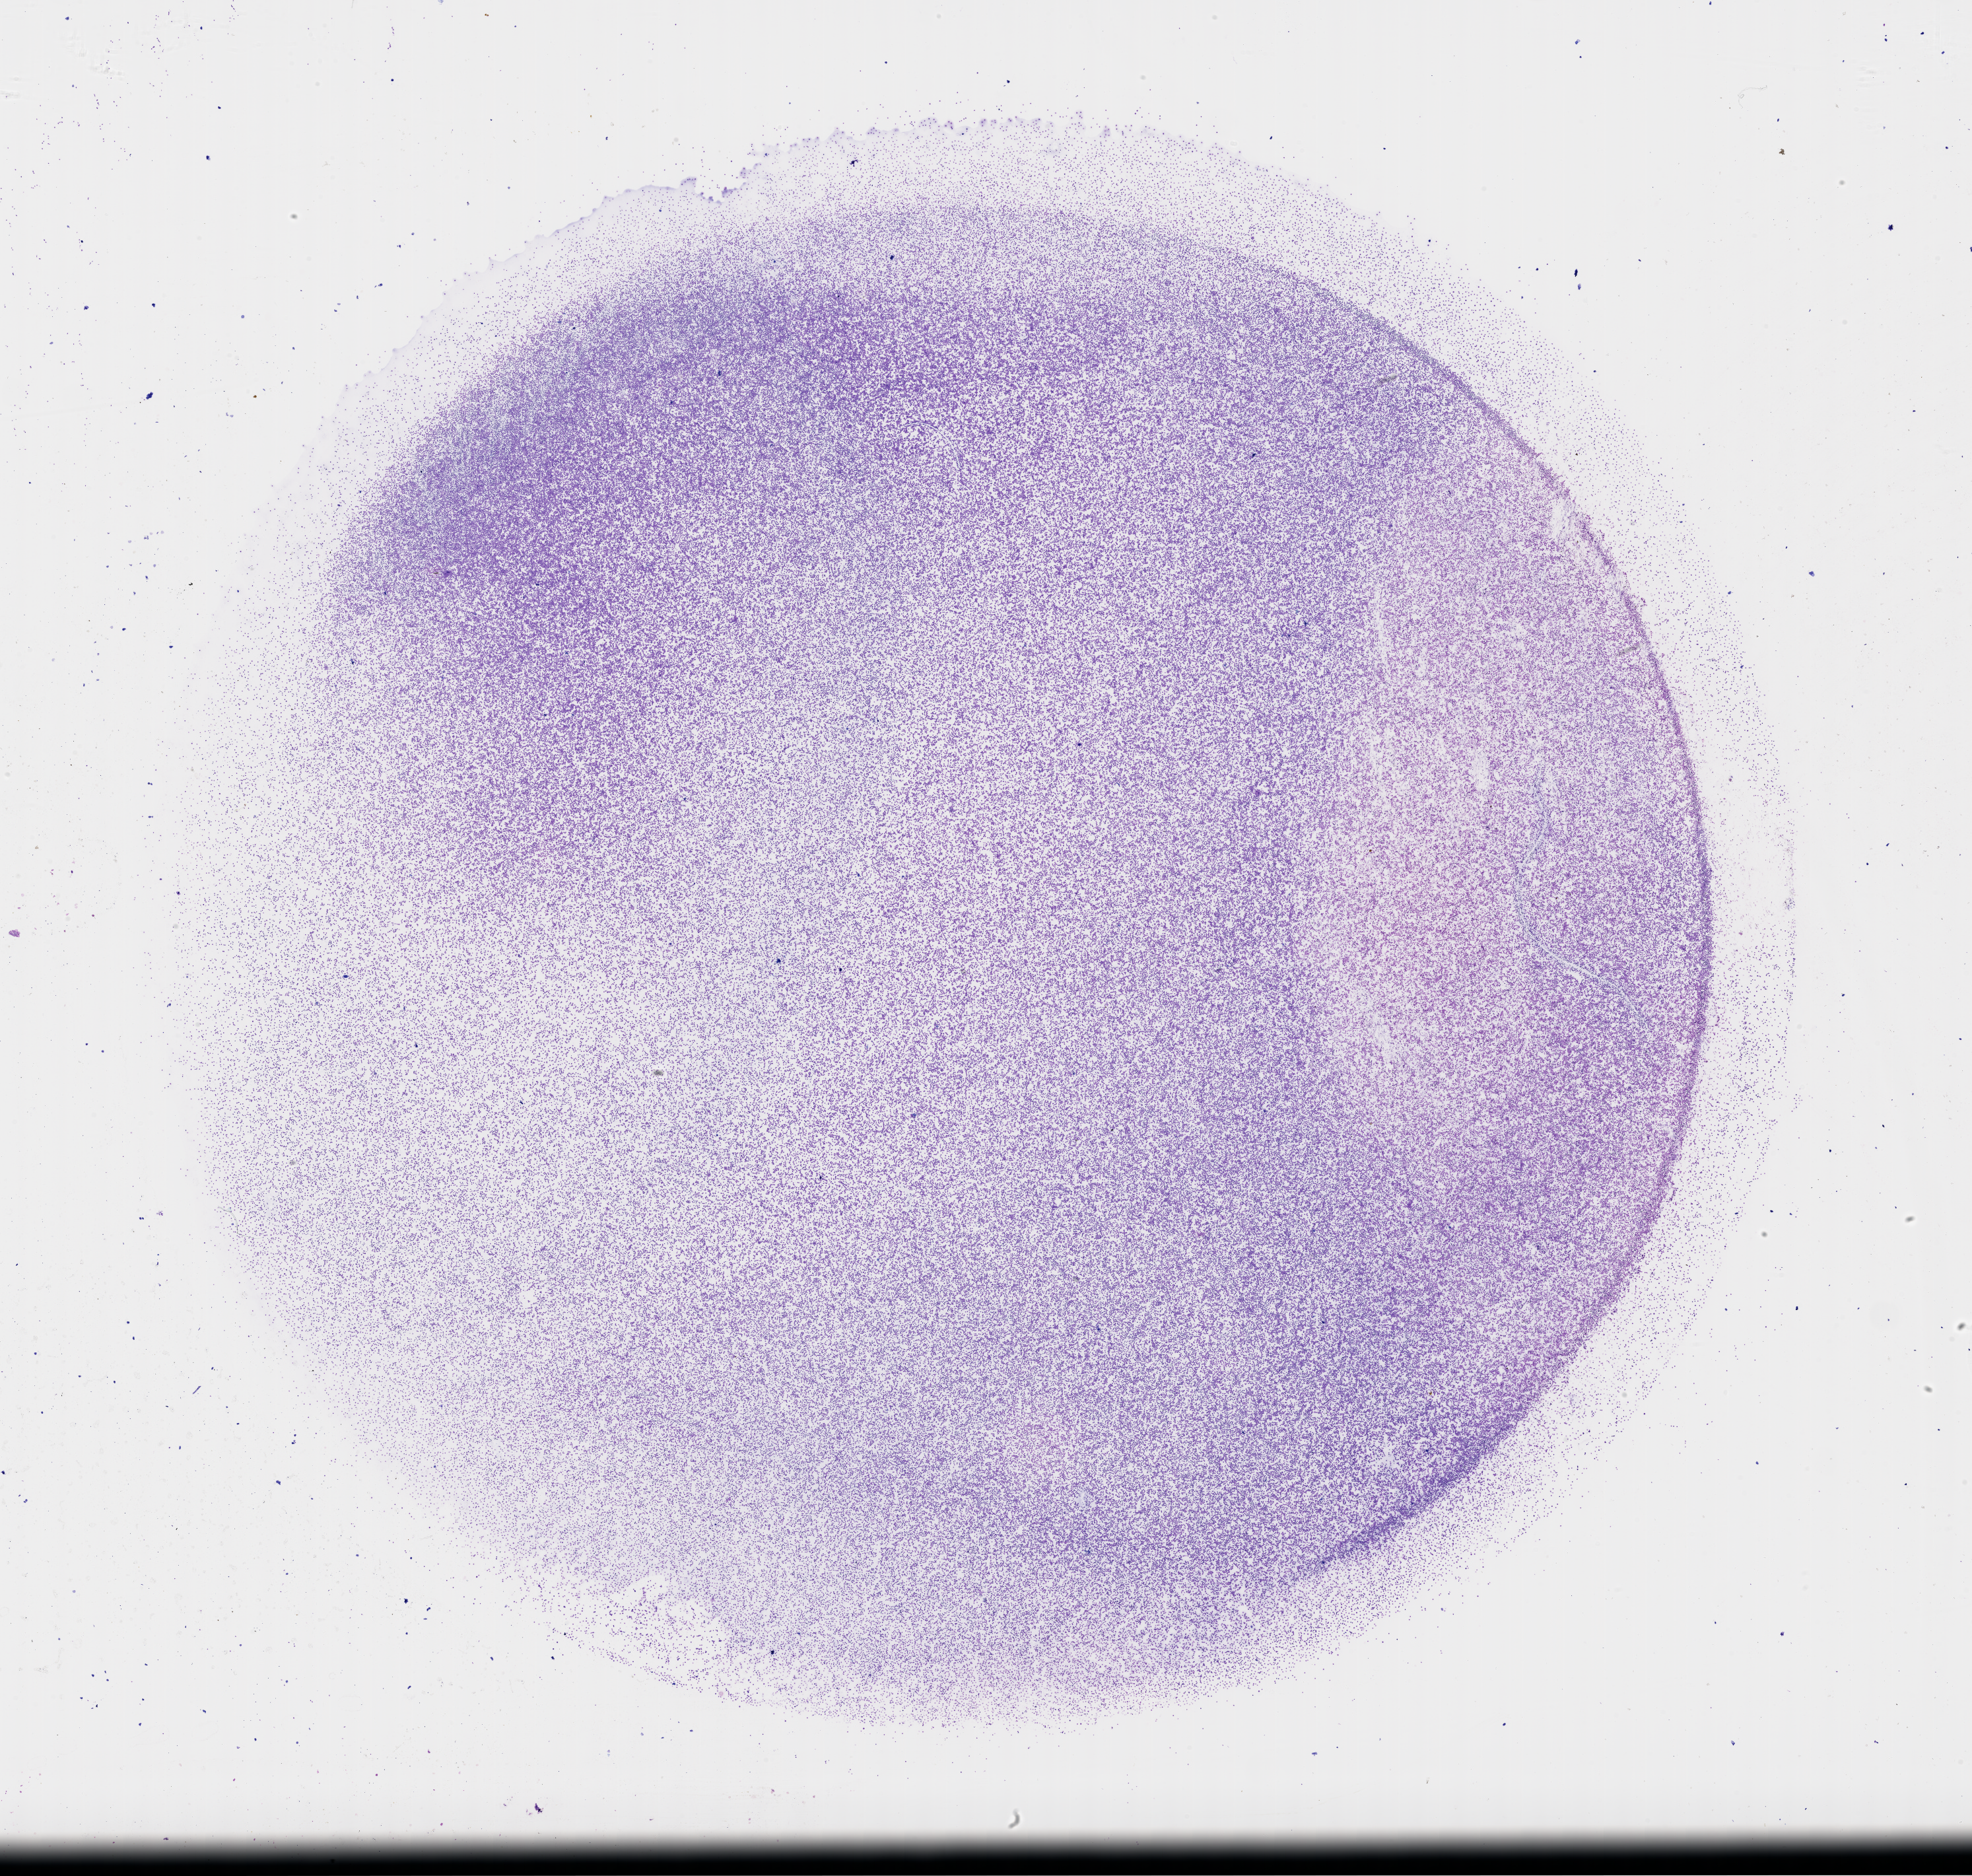
Whole-slide histology image, Hematoxylin and eosin (H&E) stained — low-resolution overview of the scanned area, about 24.1 x 22.9 mm (acquisition: 40x scan), bone marrow (leukaemic) sample. 42-year-old female patient. Blasts: 90%.
- diagnosis: Acute Myeloid Leukemia
- WHO classification: AML with maturation
- FAB classification: M2